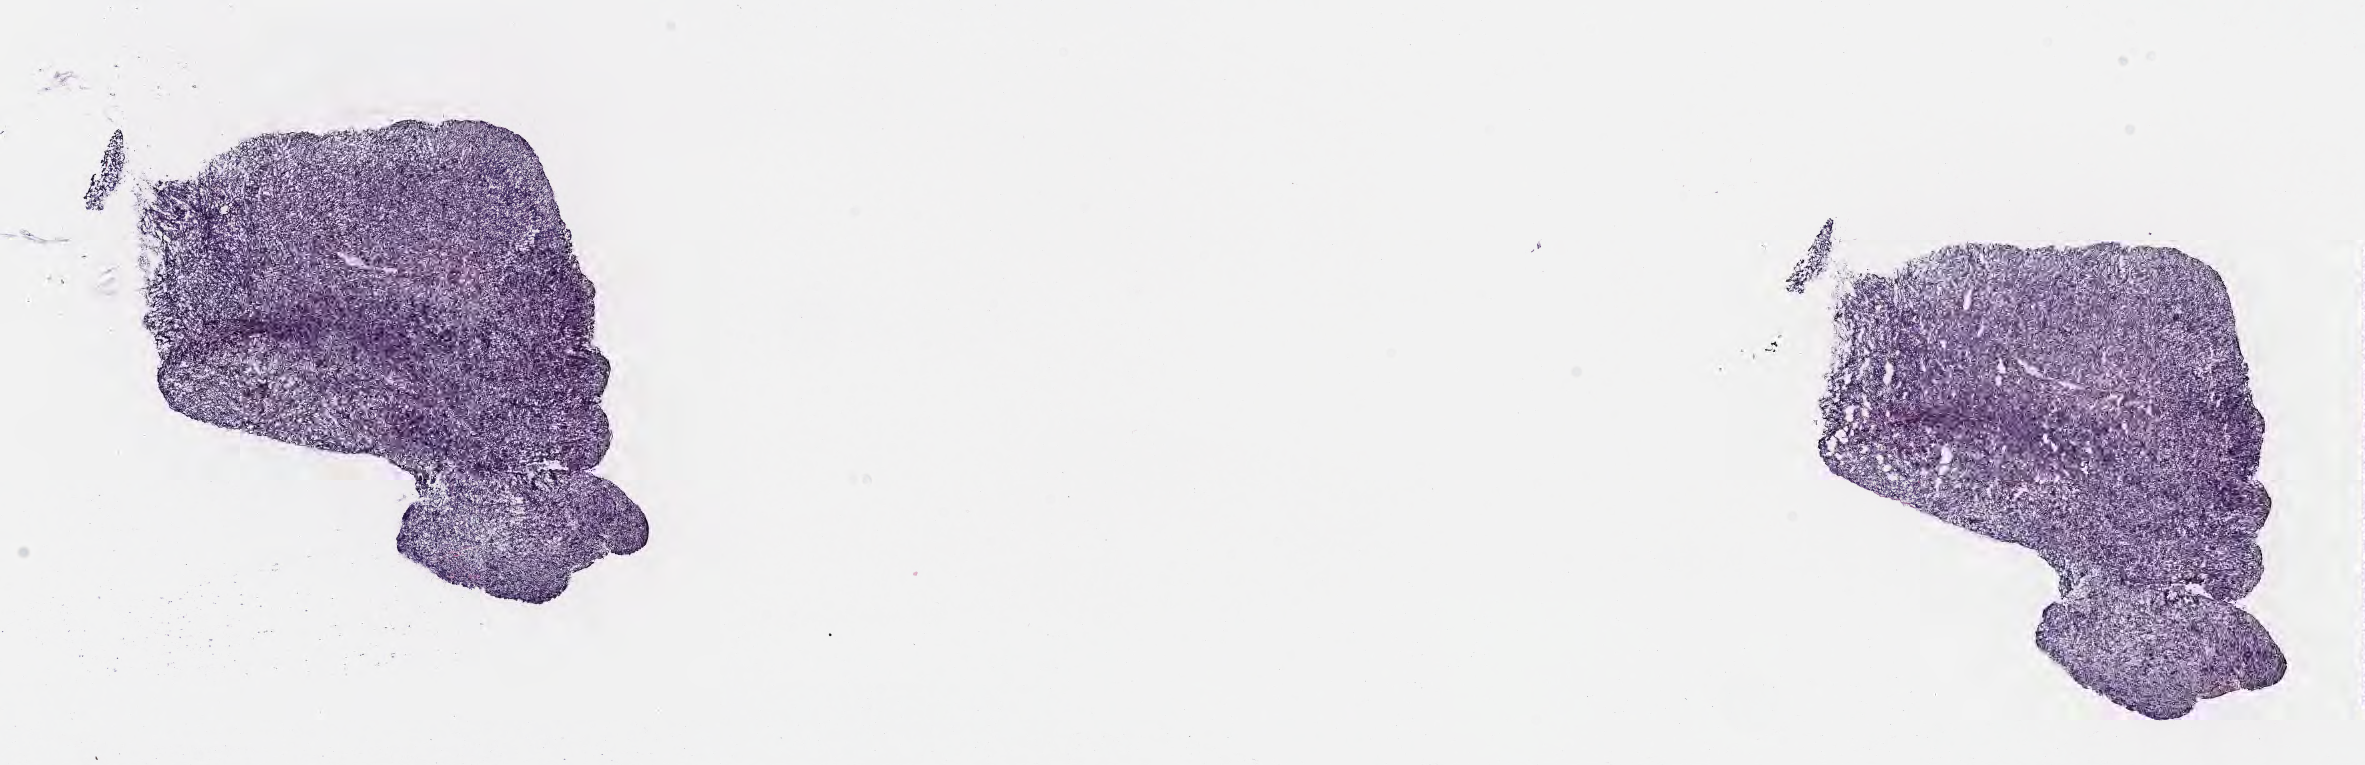
Digitized haematoxylin and eosin-stained section — a low-resolution overview of the entire scanned area, about 19.1 x 6.2 mm, frozen section (tissue freezing medium), primary tumor, anatomic site: abdomen proper. Male, age 4 years at initial diagnosis. Slide review estimates, as recorded: tumor cells 90%, tumor nuclei 90%, stromal cells 5%, necrosis 5%, normal cells 0%. Inflammatory infiltration, as recorded: lymphocyte infiltration 70%, monocyte infiltration 20%, neutrophil infiltration 0%.
- Ann Arbor stage (patient): Stage II
- diagnosis: Burkitt lymphoma, NOS
- section: top of the tissue portion